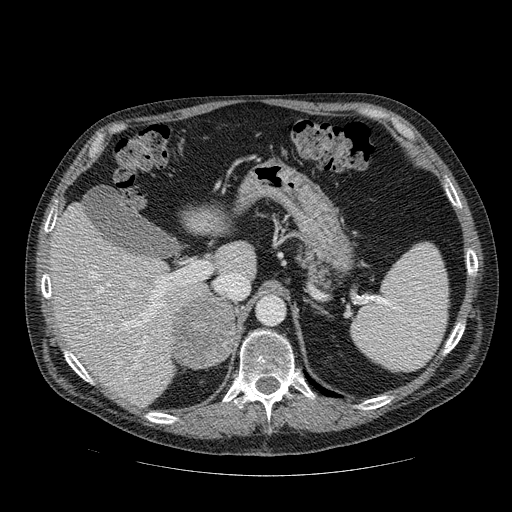
Contrast-enhanced abdominal CT, one axial slice; reconstruction kernel STANDARD; 120 kVp; soft-tissue window (W 400 / L 40 HU); 512 × 512 image matrix, field of view 420 × 420 mm. Patient: male, 56 years. From the clinical record (not read from this slice): diagnosis: adrenocortical carcinoma; tumour side: right adrenal; tumour size at pathology: 9 cm; Ki-67 index: 48 %; stage (as recorded): 4.
Annotated regions visible in this slice (semi-automatic segmentation, software-assisted and operator-edited):
- mass: bounding box (x1, y1, x2, y2) in pixels: (171, 293, 235, 367)